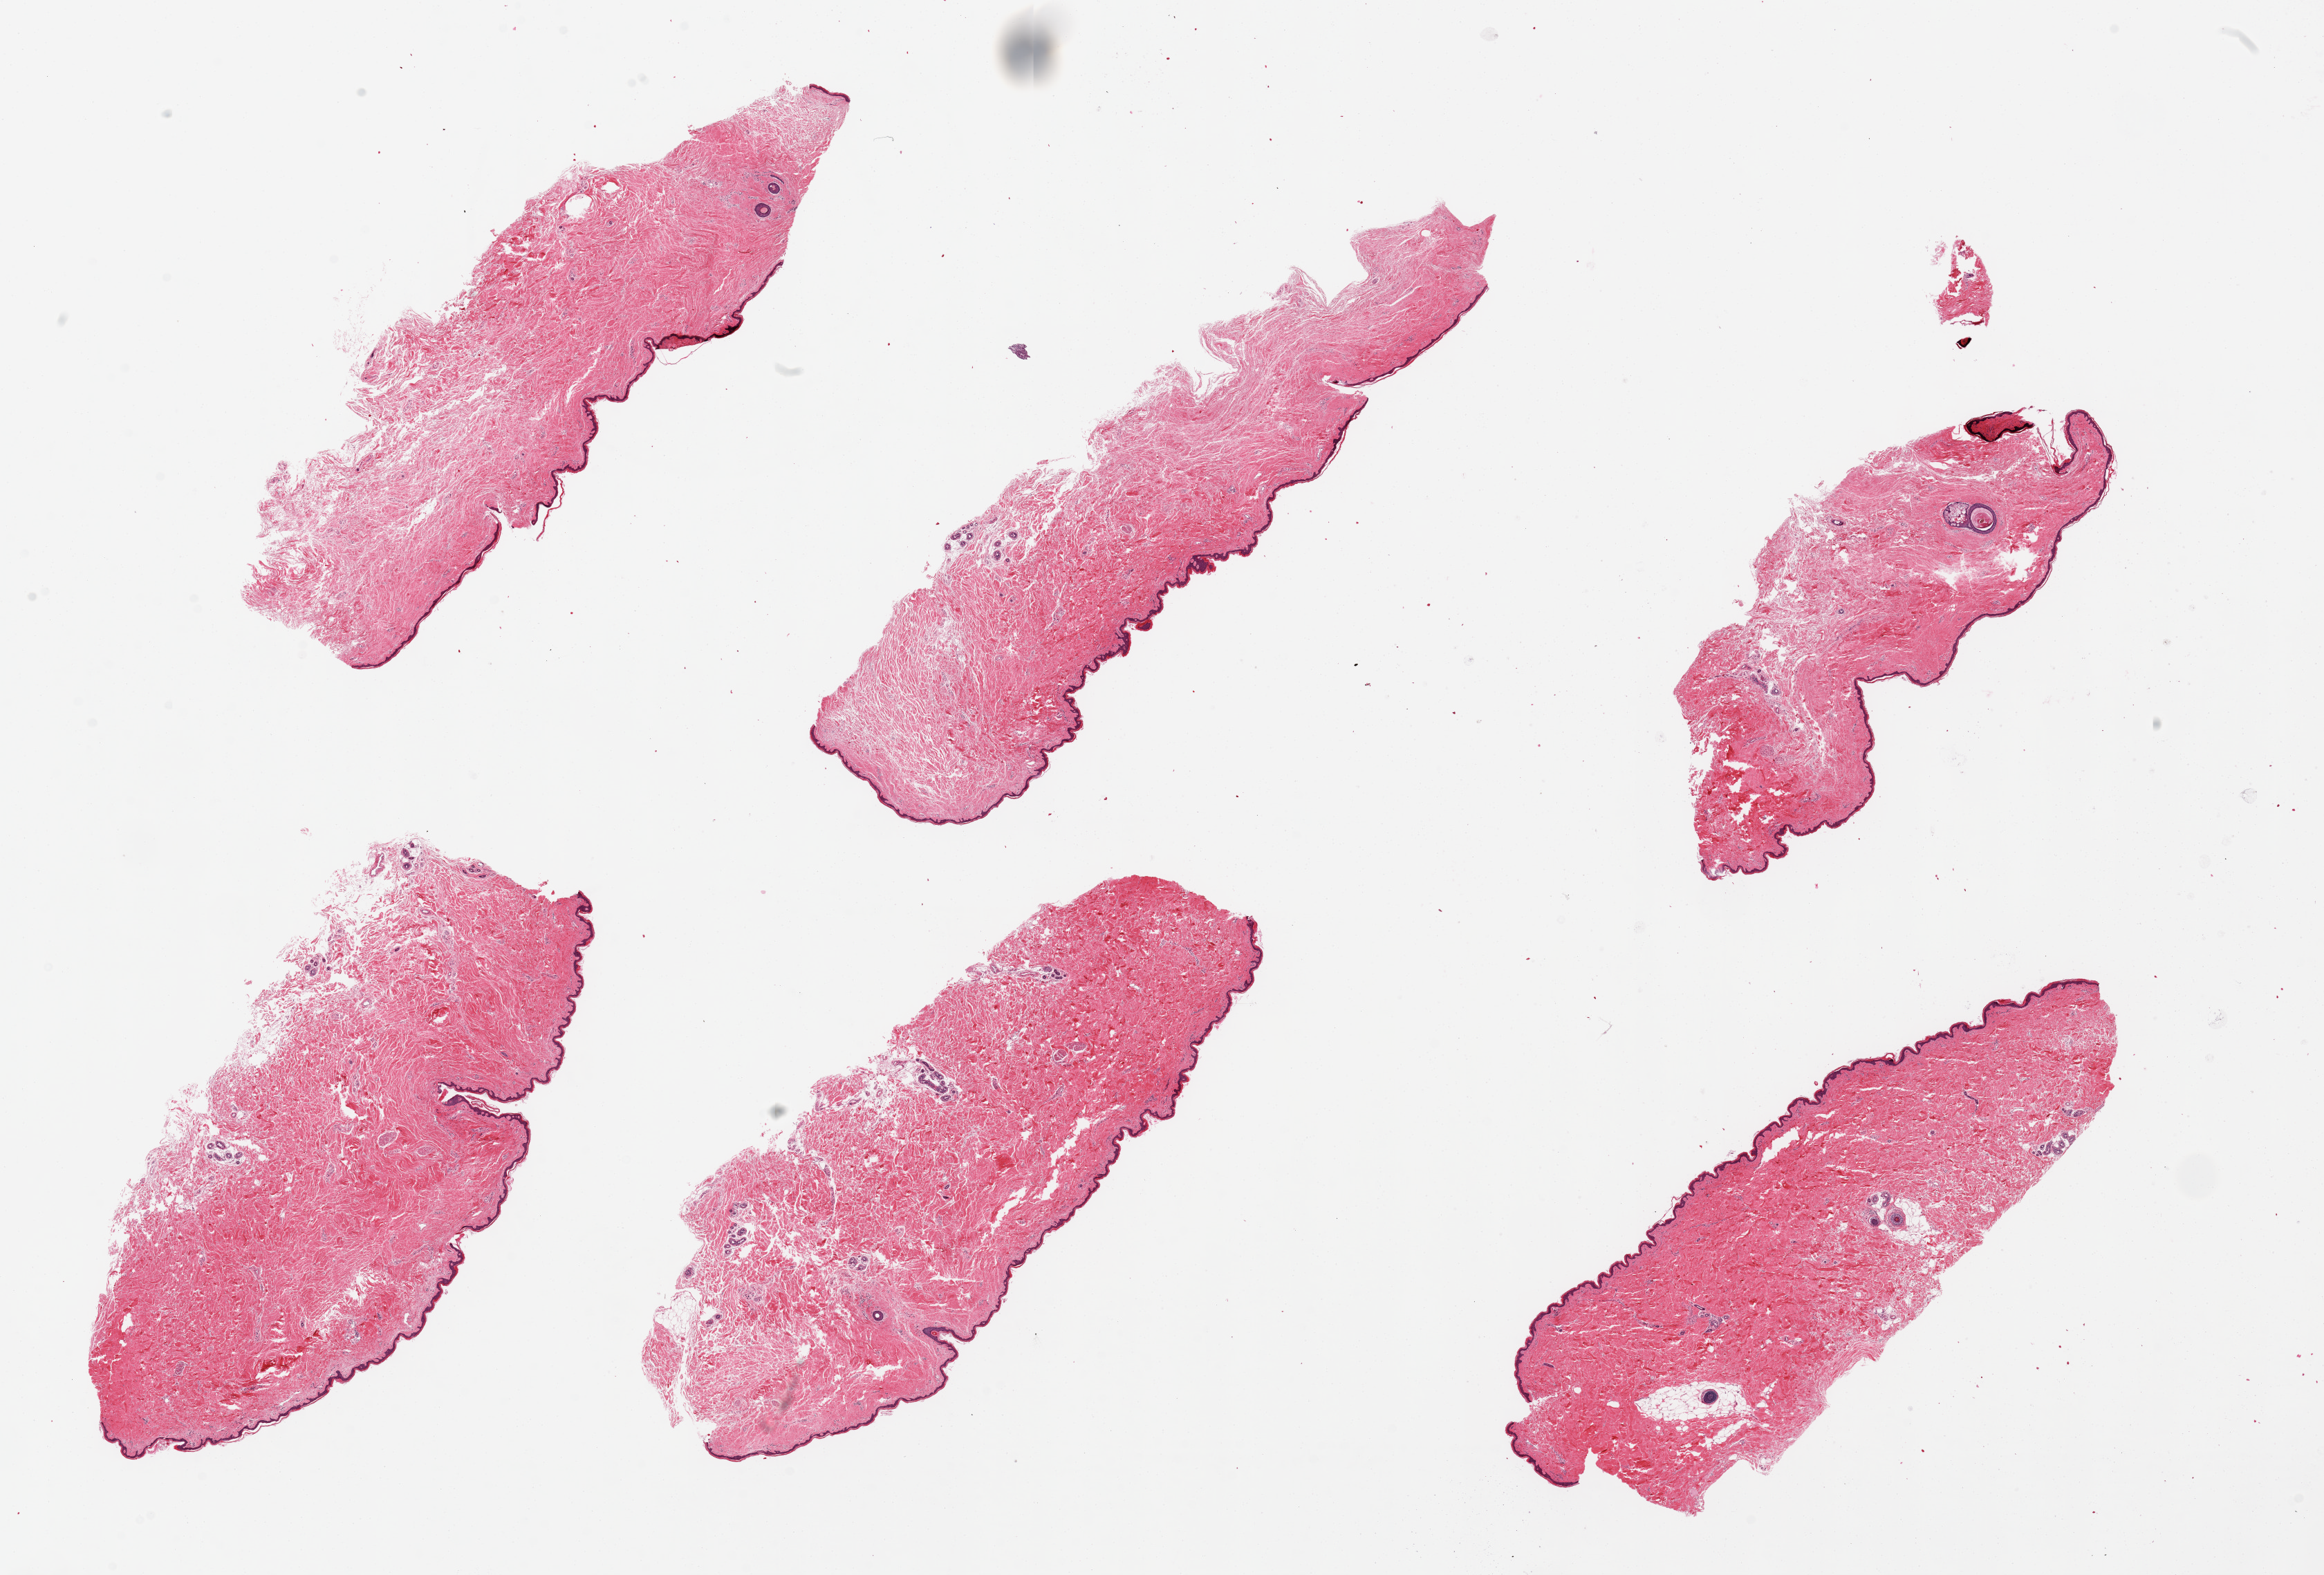
Hematoxylin and eosin (H&E) whole-slide image — whole scanned area (about 26.6 x 18.0 mm, from a 20x scan) shown as a low-resolution overview. PAXgene-fixed, paraffin-embedded tissue. Target tissue: skin of suprapubic region. Tissue donor sample.
* reviewer comment on this tissue sample: 6 pieces, up to 10x3mm; squamous epithelium ~1% thickness